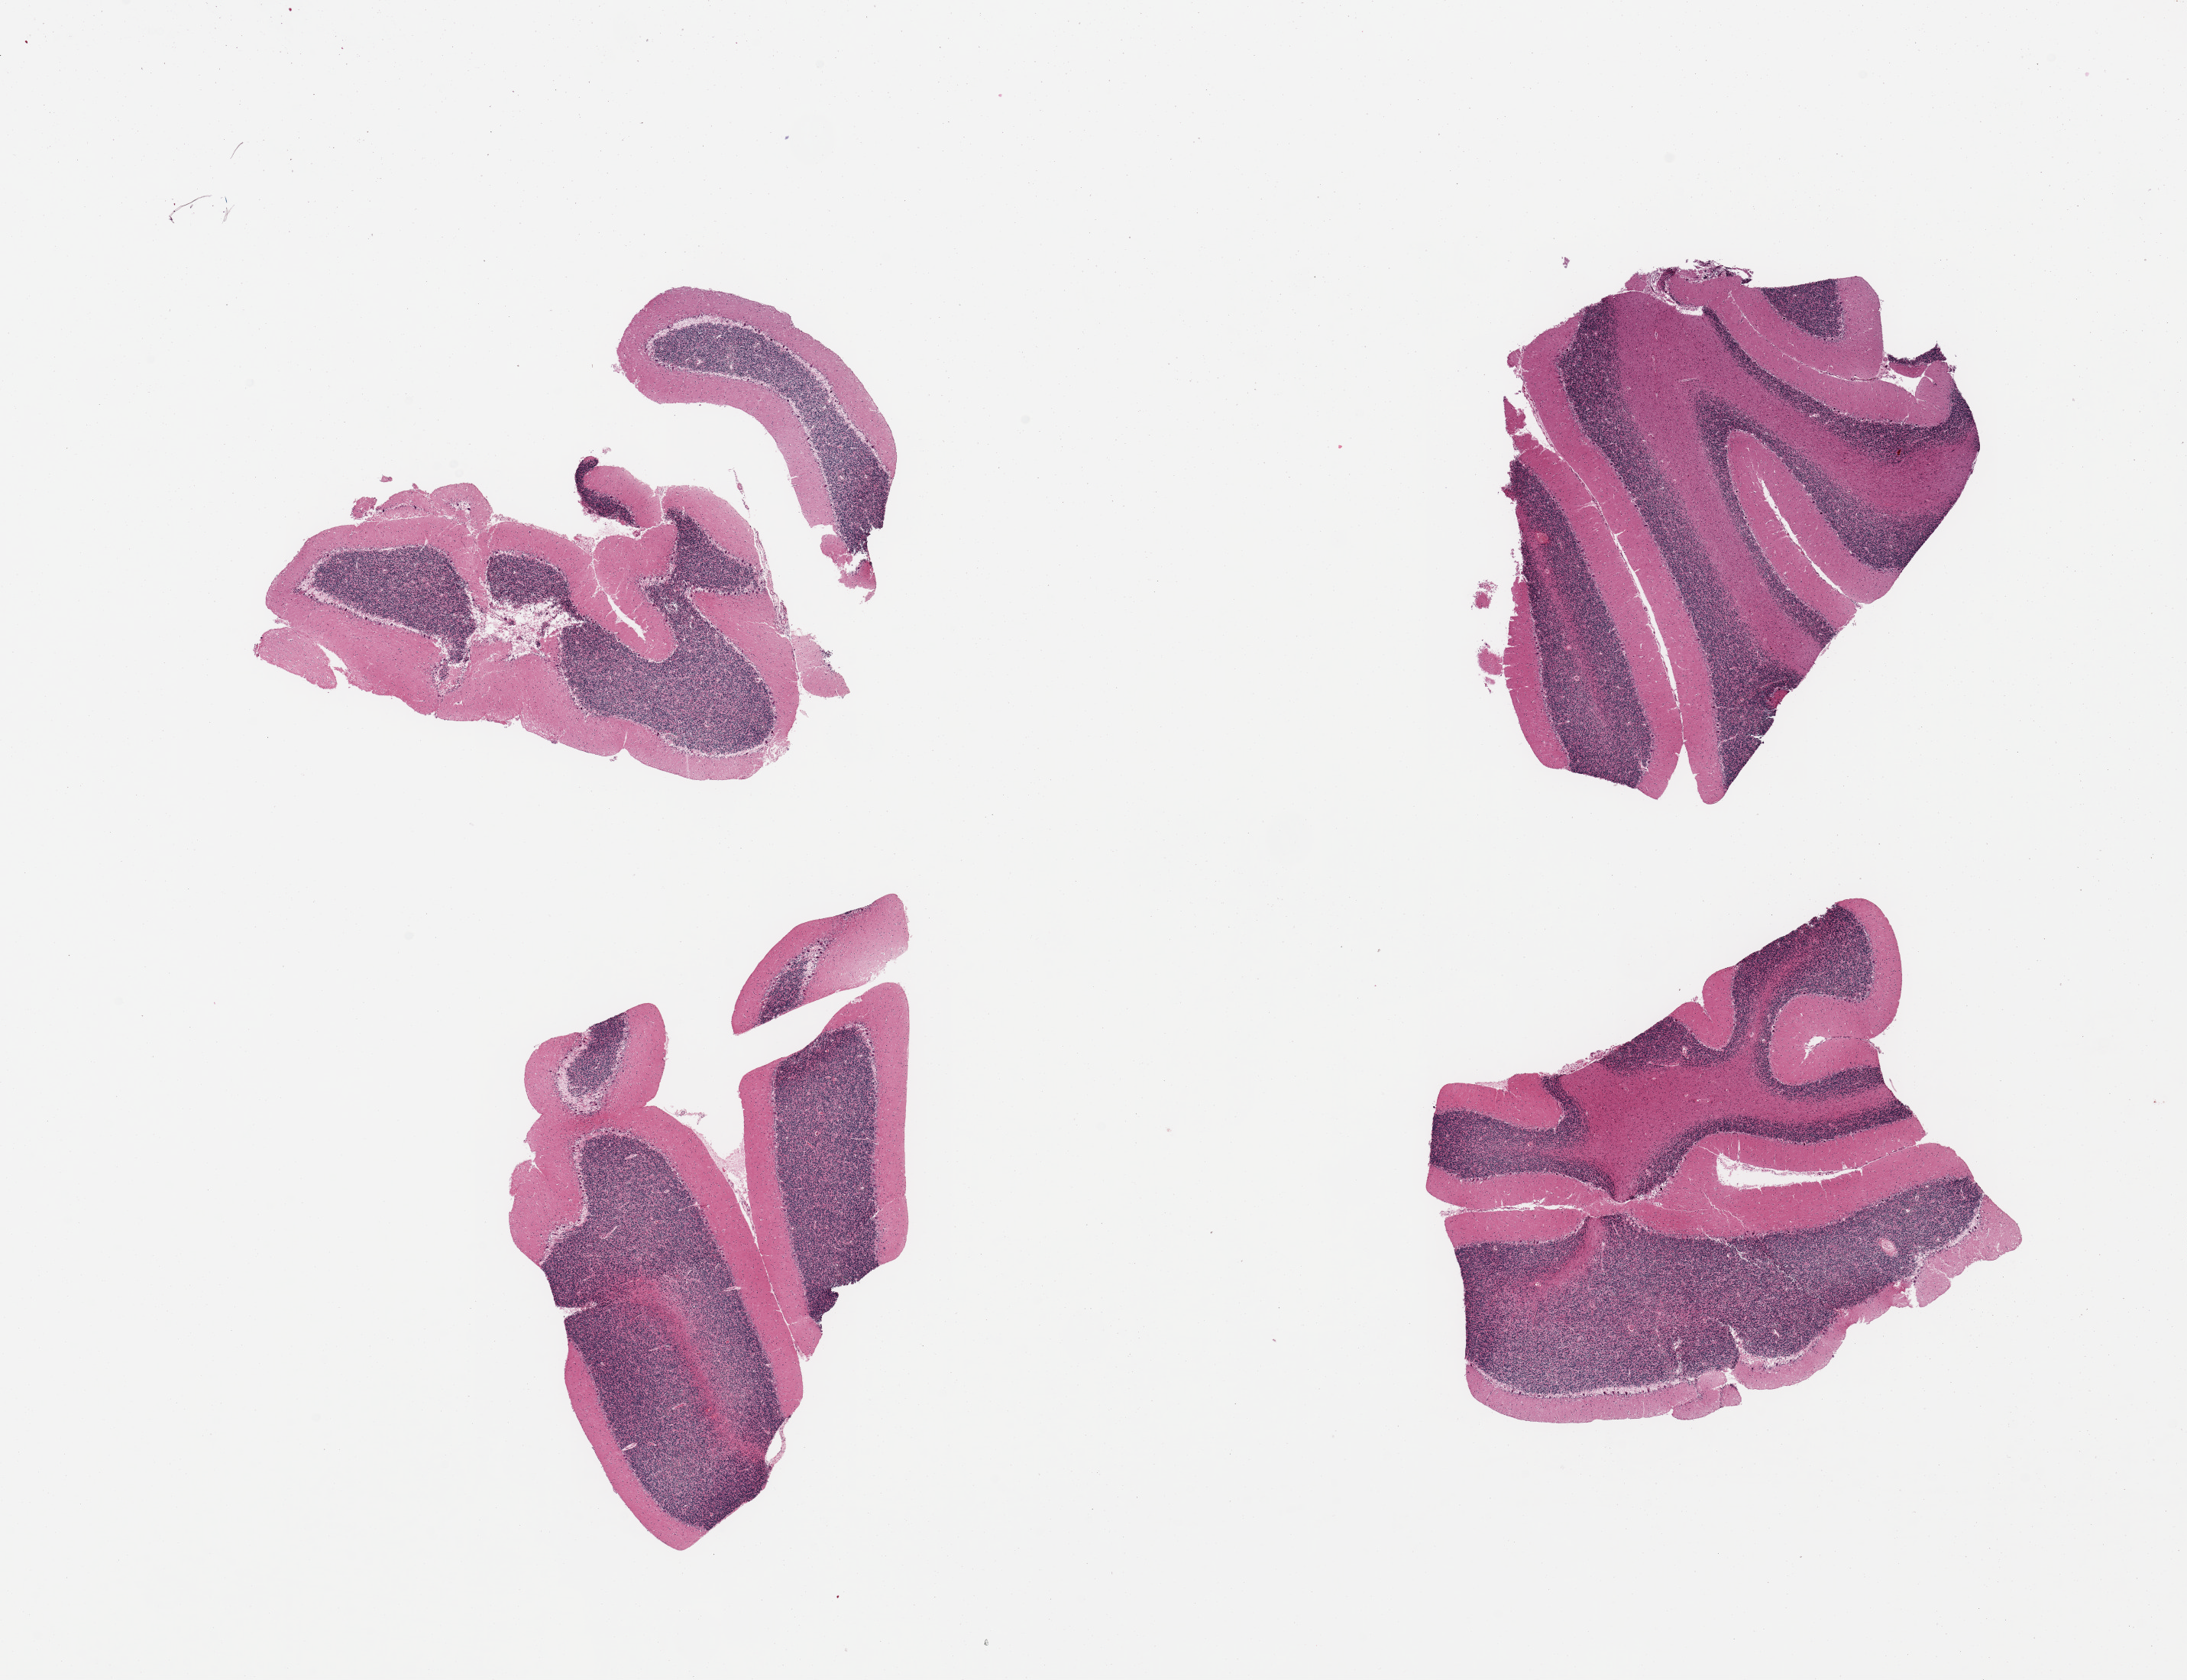
Whole-slide image, hematoxylin and eosin (H&E) stain, shown as a low-resolution overview of the whole scanned area (about 22.6 x 17.4 mm, from a 20x scan), PAXgene-fixed paraffin-embedded (PFPE) section, target tissue: cerebellum, donor tissue sample. Donor: male.
Reviewer comment on this tissue sample: 4 pieces; Purkinje cells well visualized.